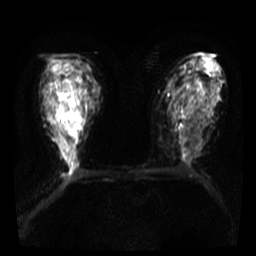
Breast MRI, one axial slice. Slice 21 of 36 in the series (ordered by position). Diffusion-weighted series; image 2 of 4 stored at this slice position (different b-values; order by instance number). 3 T. 5 mm slice thickness. 256 × 256 image matrix. Female patient.
Structures marked on this image (outlined manually by an expert reader):
- tumour on diffusion-weighted imaging: box from (x=60, y=82) to (x=73, y=93) px